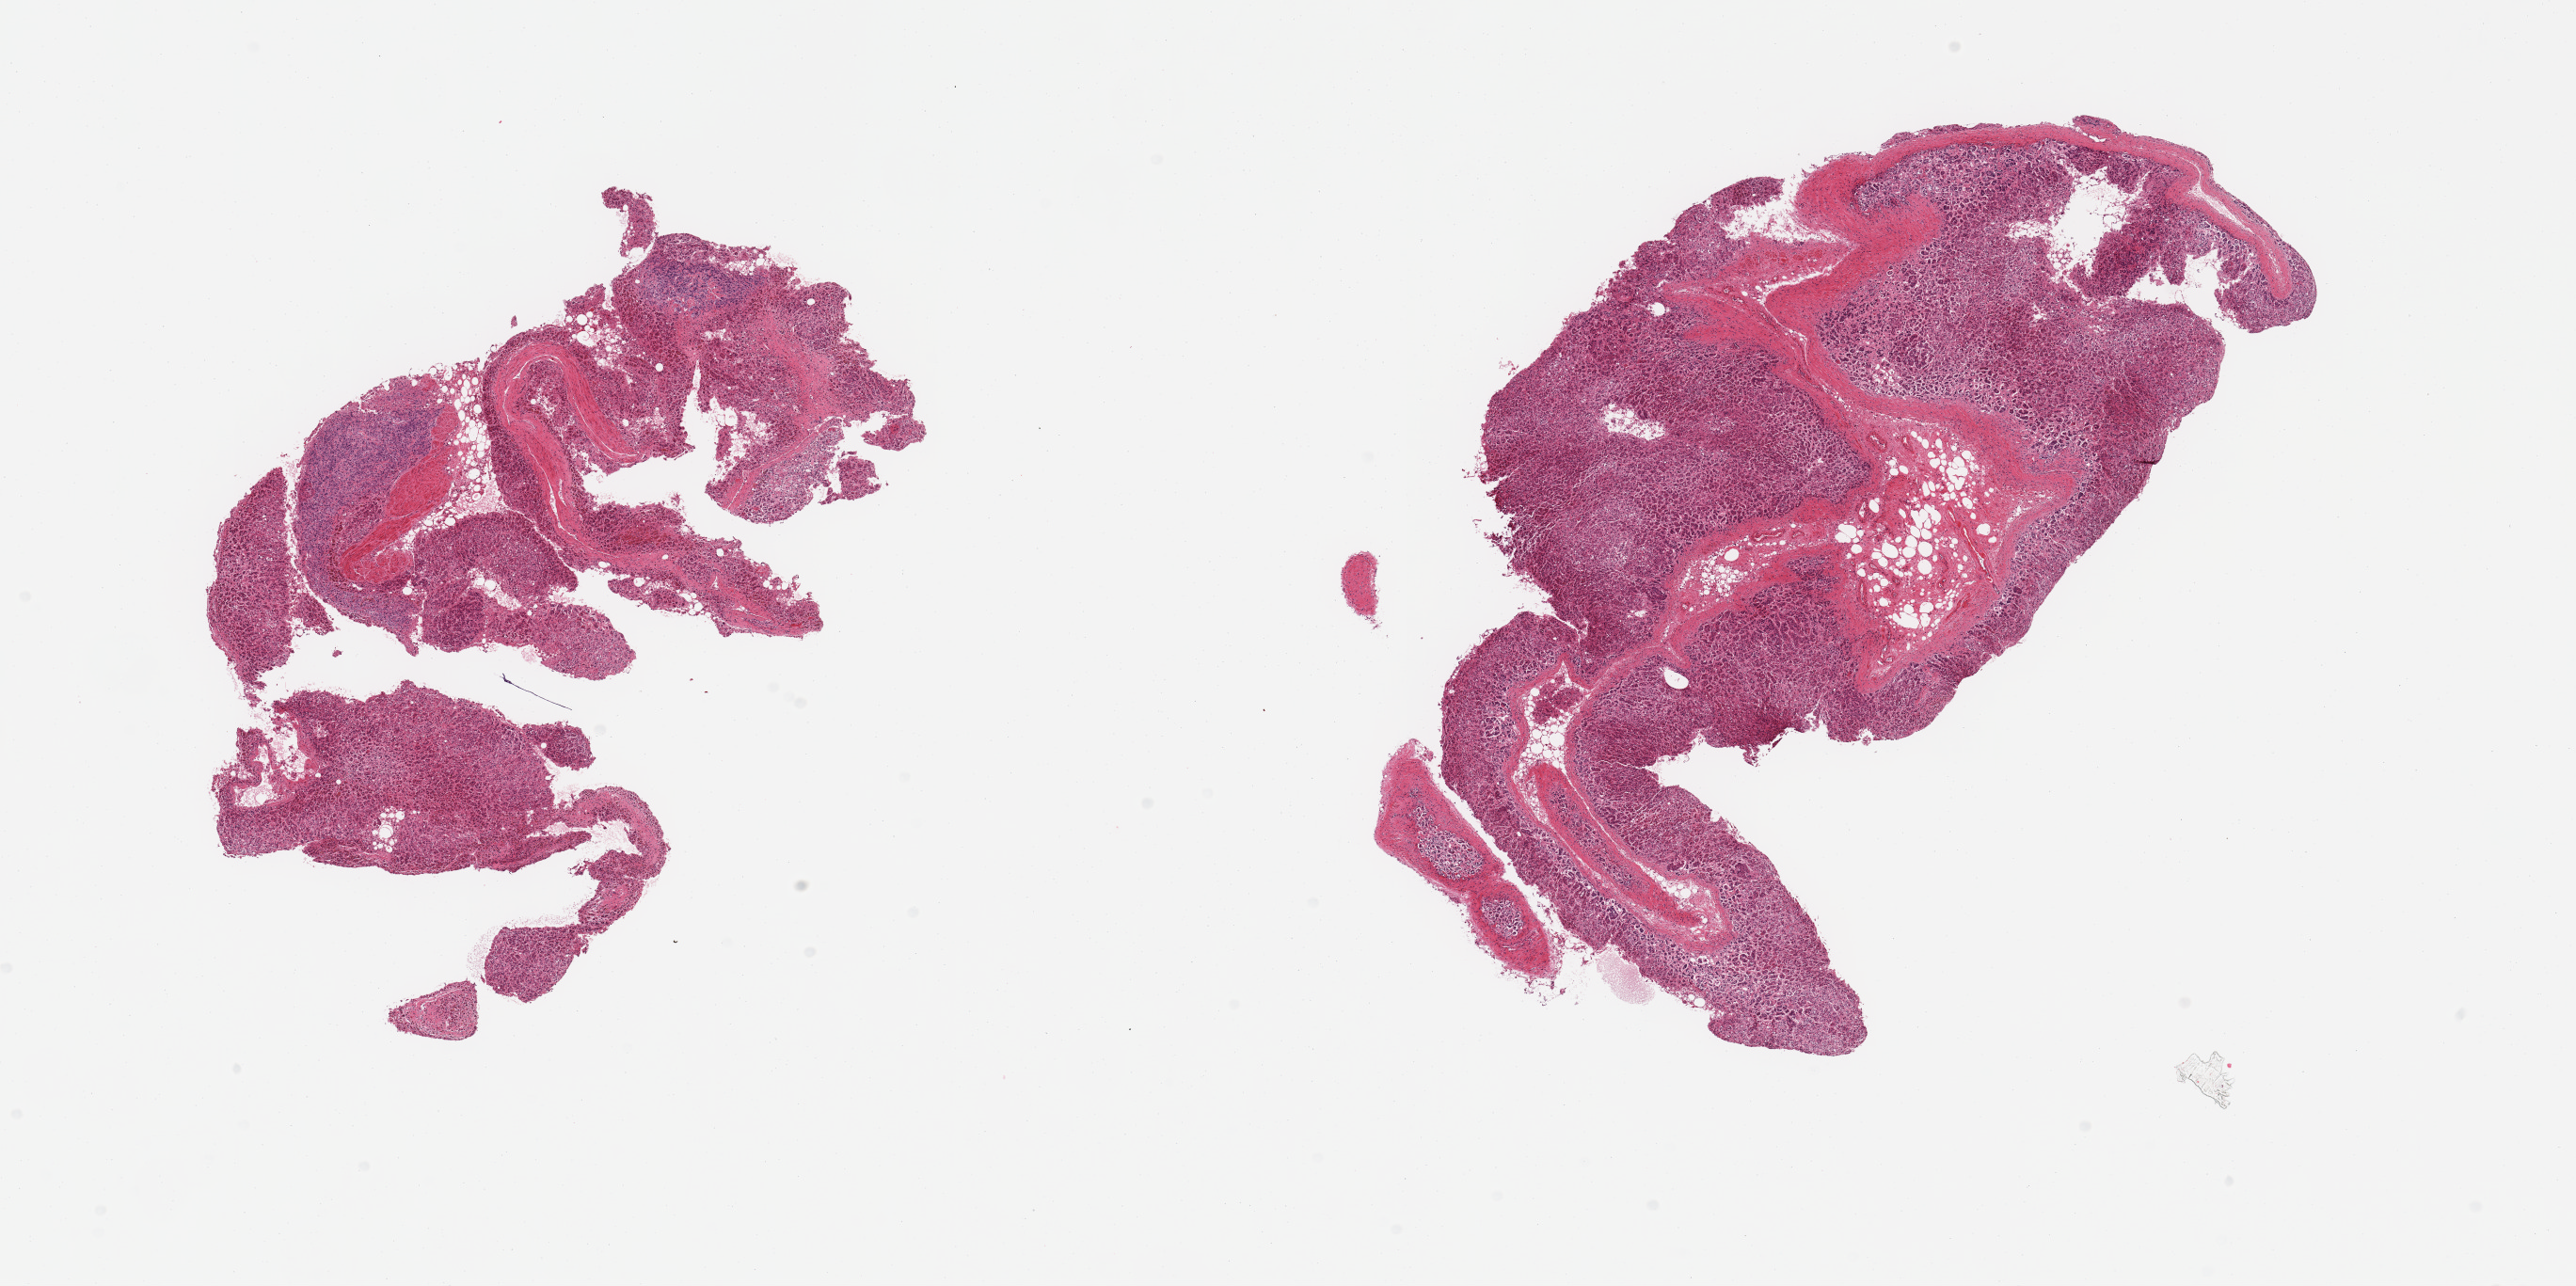
Whole-slide image, haematoxylin and eosin stain — low-resolution overview of the scanned area, about 21.7 x 10.8 mm (slide scanned at 20x); PAXgene-fixed paraffin-embedded (PFPE) section; section of adrenal gland (target tissue); donor tissue sample.
Pathologist's review note for this sample: 2 pieces, cortex.